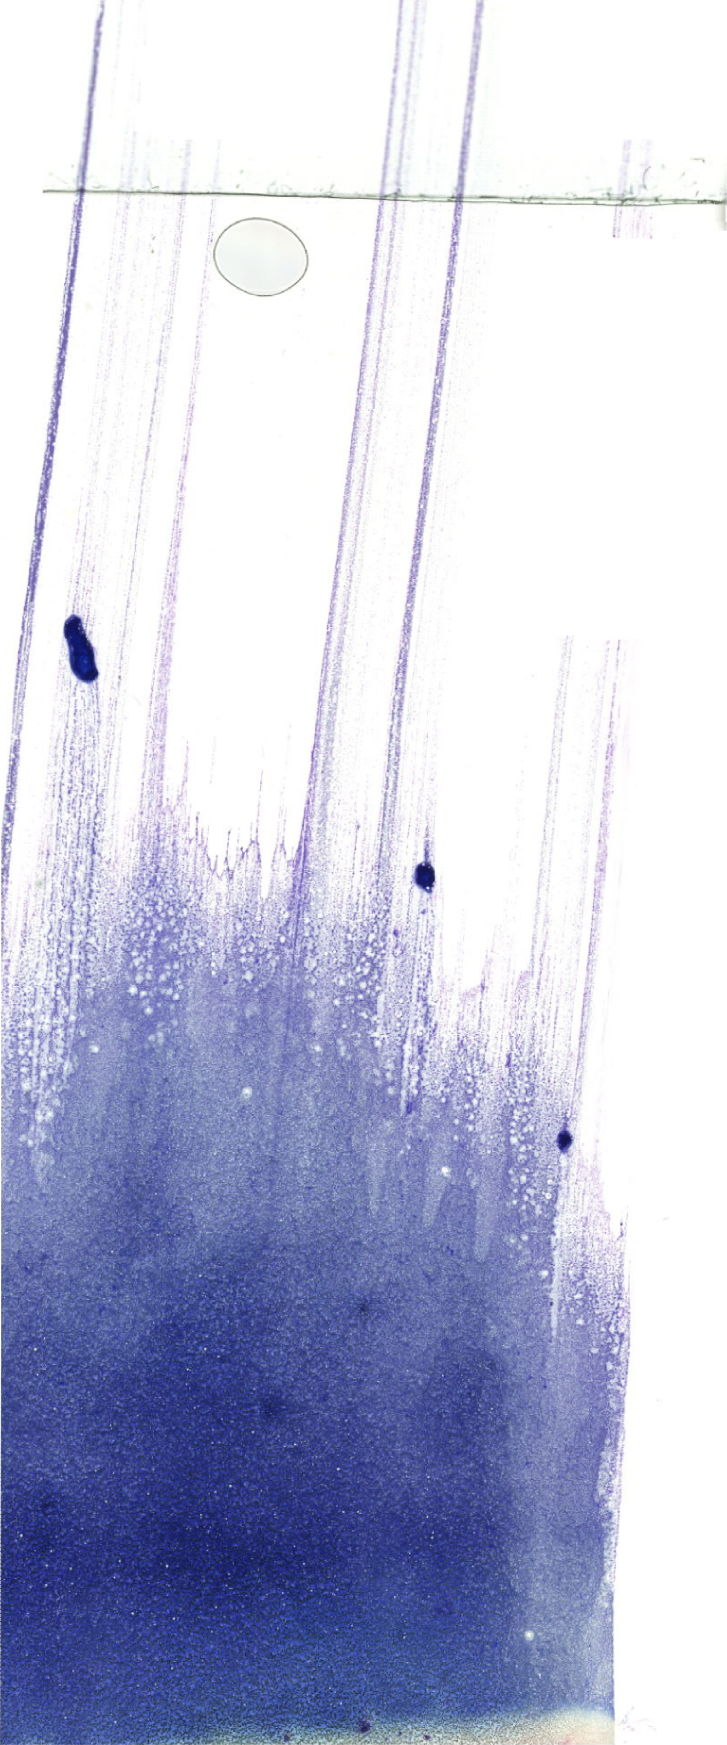
May-Grünwald–Giemsa-stained marrow aspirate smear (whole slide) — whole scanned area (about 20.6 x 49.5 mm) shown as a low-resolution overview. Male patient.
Diagnosis: B Acute Lymphoblastic Leukemia.